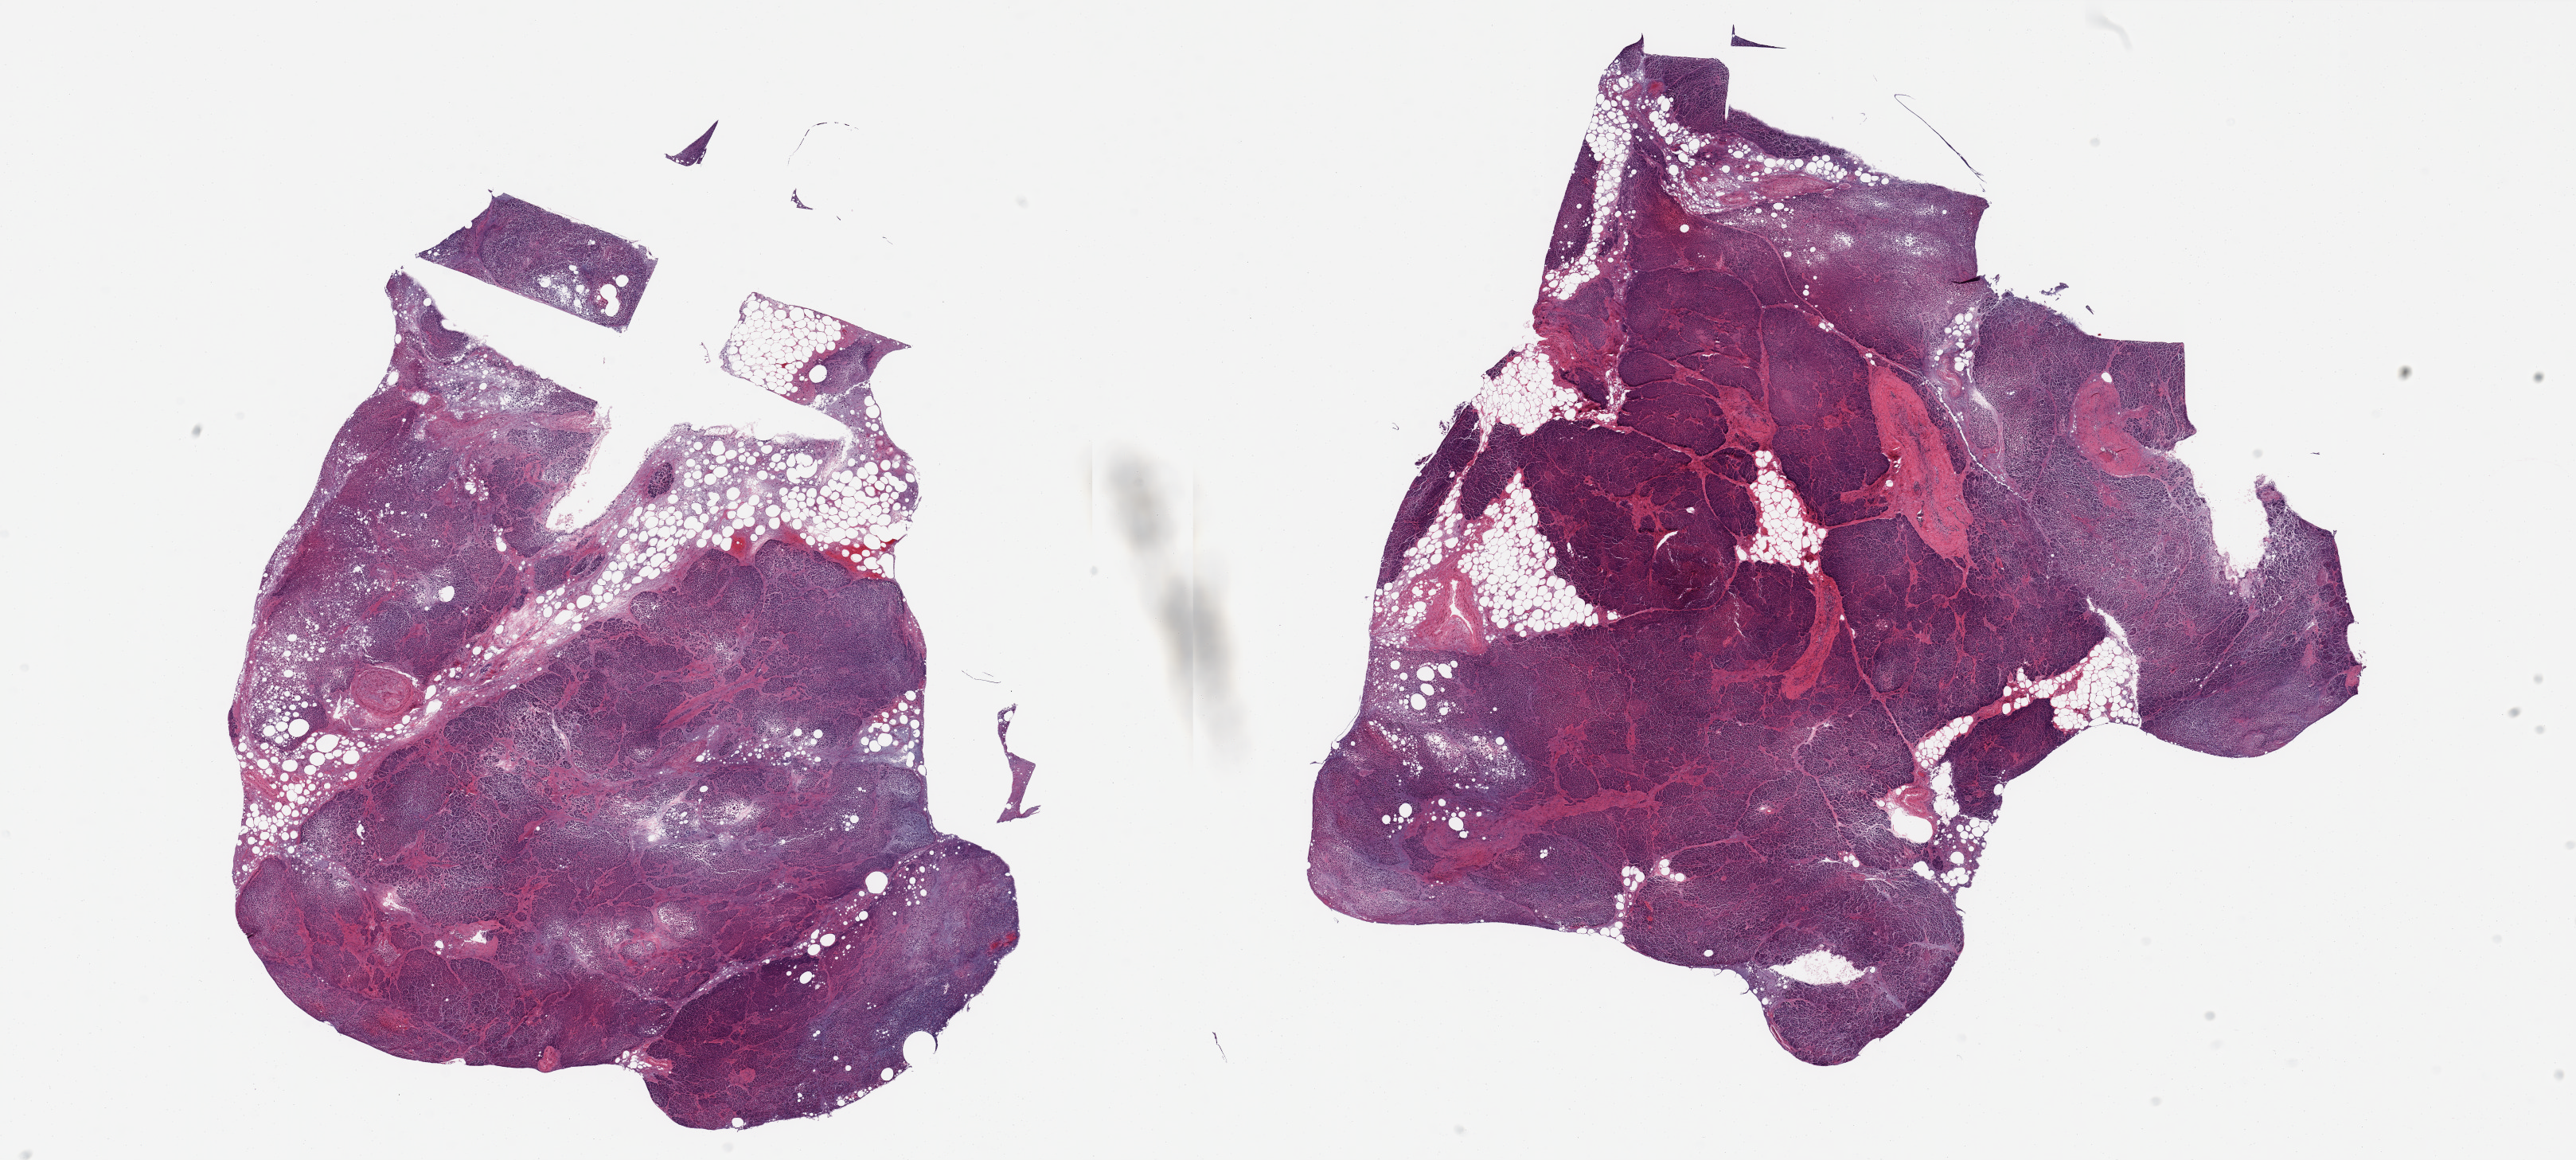
Hematoxylin and eosin (H&E) whole-slide image, a low-resolution overview of the entire scanned area, about 25.6 x 11.5 mm (from a 20x scan), PAXgene-fixed paraffin-embedded (PFPE) section, sampled site (target tissue): pancreas, tissue donor sample. Donor: male.
Reviewer comment on this tissue sample: 2 pieces; about a third is severely autolyzed; 10% internal fat.